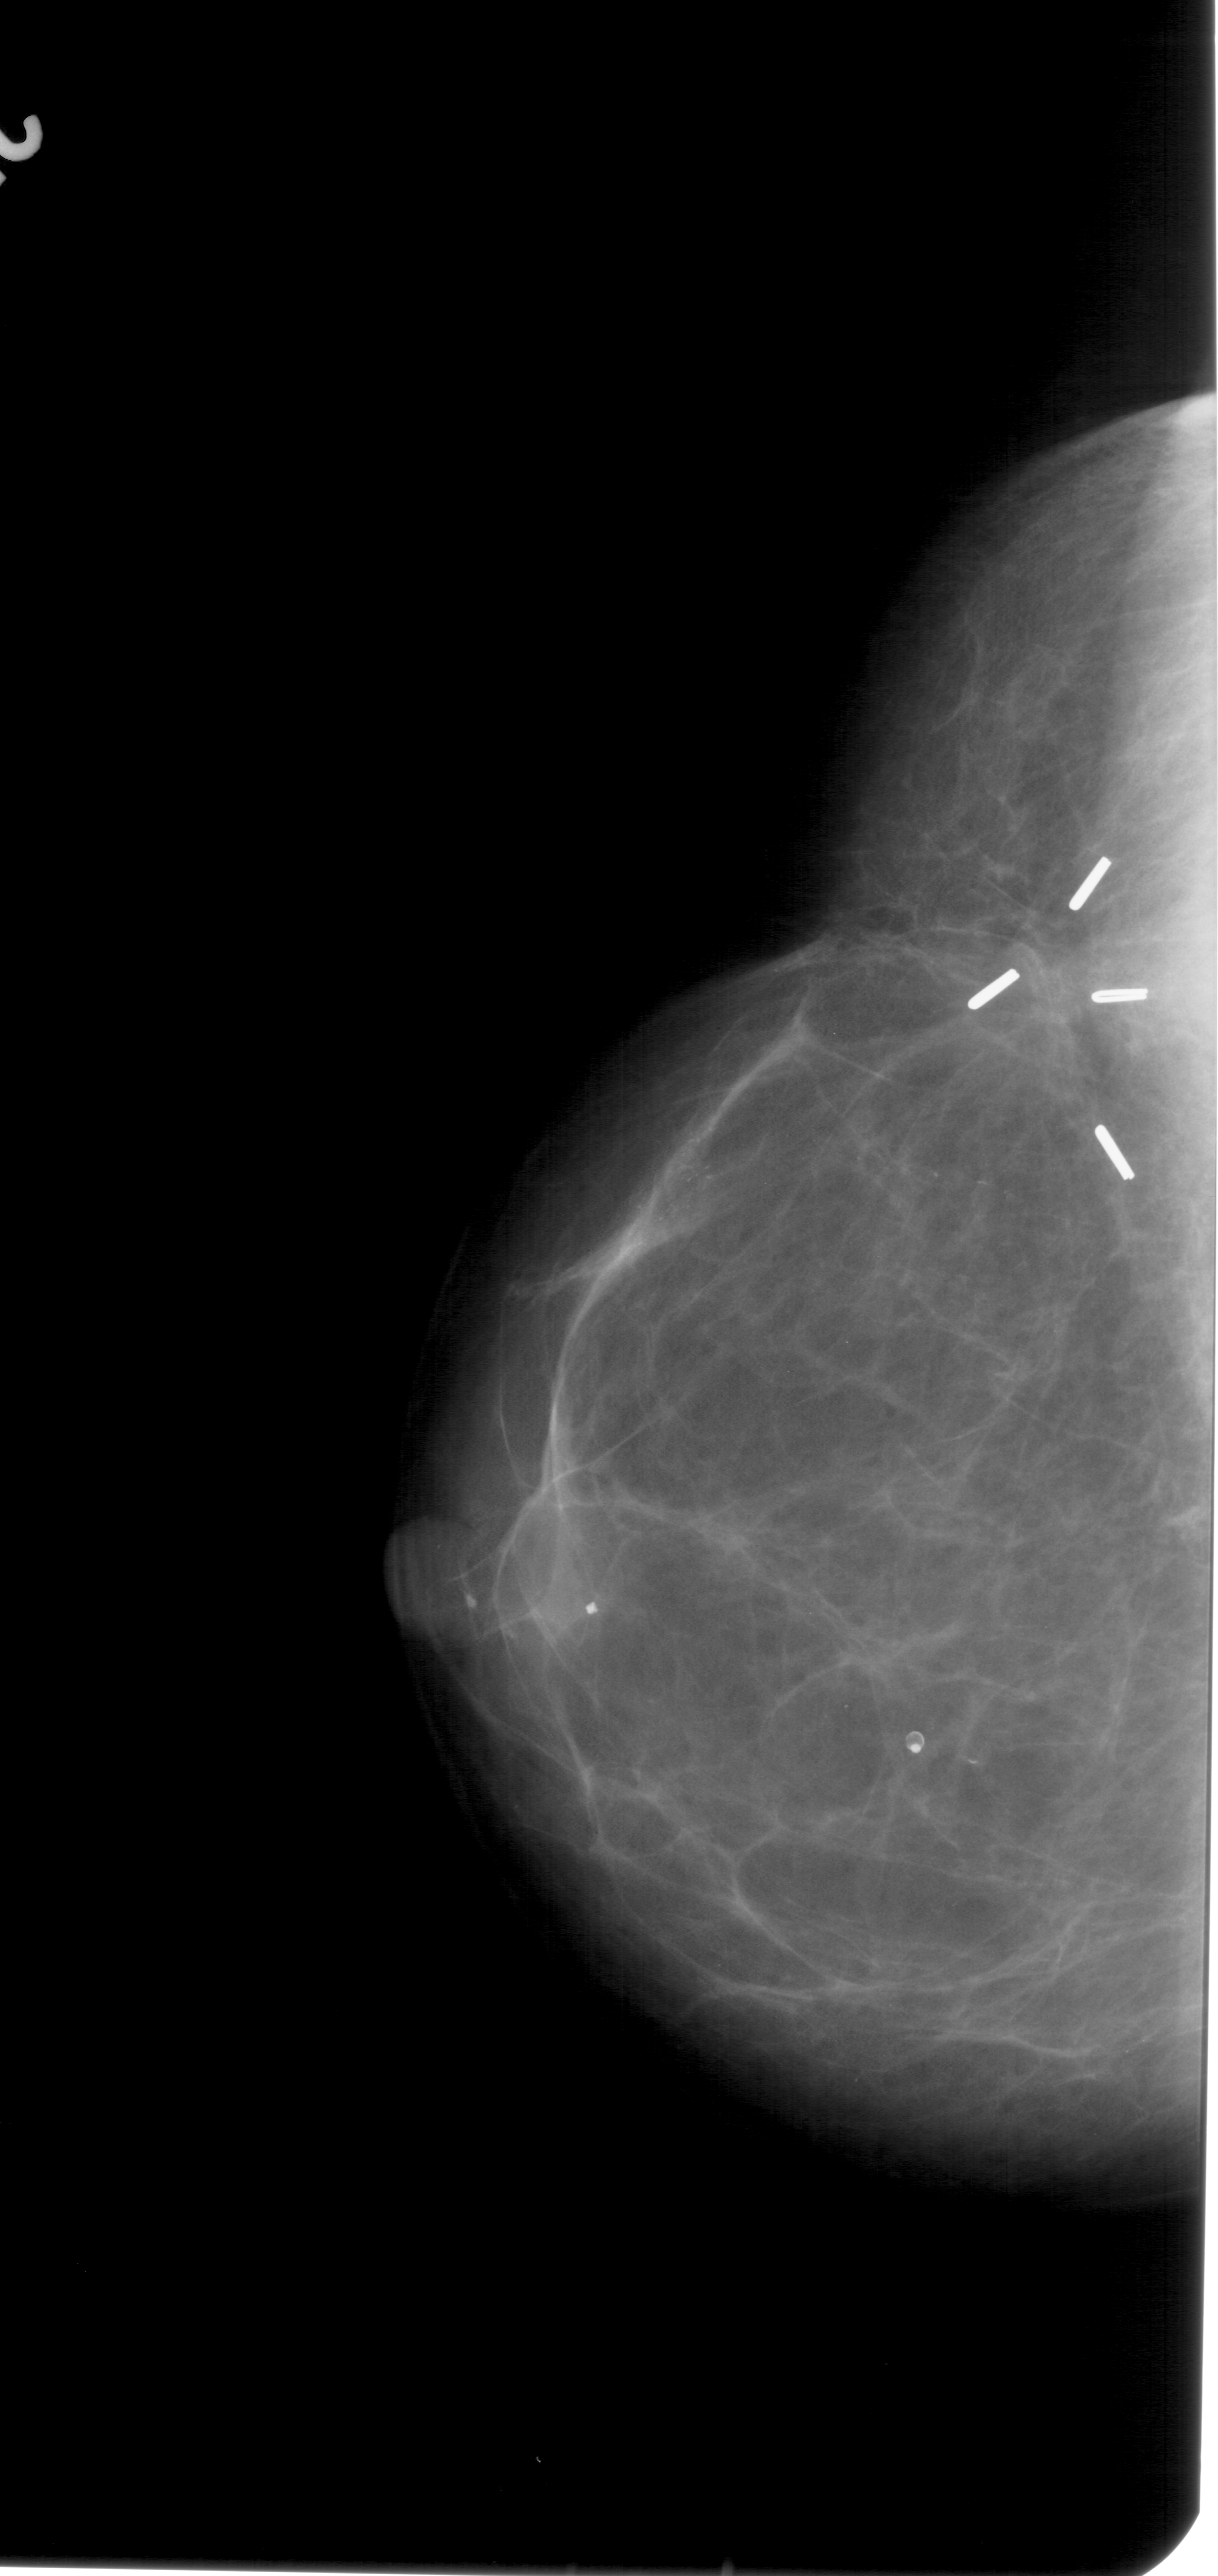
Mammogram (digitized film). Left breast. Craniocaudal (CC) view. Breast composition: heterogeneously dense (BI-RADS density category 3 of 4). 1218 × 2576 image matrix.
Marked abnormalities (boxes around the expert regions of interest):
- calcifications, morphology pleomorphic, distribution linear; BI-RADS assessment category 5; subtlety rating 4 on a 1 (subtle) to 5 (obvious) scale; pathology result (as recorded, not read from the image): malignant: box from (x=535, y=939) to (x=1036, y=1332) px